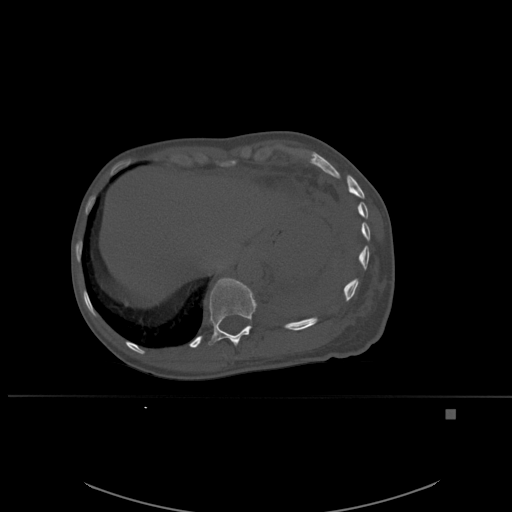
CT including the spine, one axial slice. Bone window (W 1800 / L 400 HU). 1.5 mm slice thickness. 512 × 512 image matrix. Female patient, age 45 years. Case-level facts recorded for this patient, not image findings: primary cancer: lung.
Annotated regions visible in this slice (semi-automatically segmented with operator editing):
- T11 vertebra: bounding box <208,278,257,346> (left, top, right, bottom; pixels)